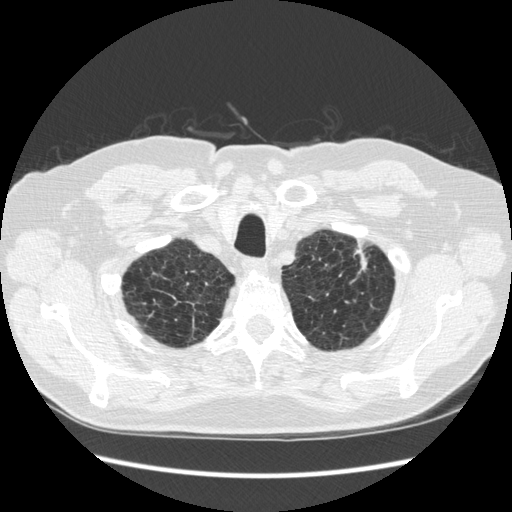
Low-dose screening chest CT, one axial slice. Position 239 of 267 along the scan axis. Reconstruction kernel STANDARD. Lung window (W 1500 / L -600 HU). 1.25 mm slice thickness. 512 × 512 image matrix, field of view 360 × 360 mm.
Structures marked on this image (outlined manually by an expert reader):
- lesion 1 (tumor, upper lobe of left lung): bounding box [x1, y1, x2, y2] px = [354, 249, 367, 273]